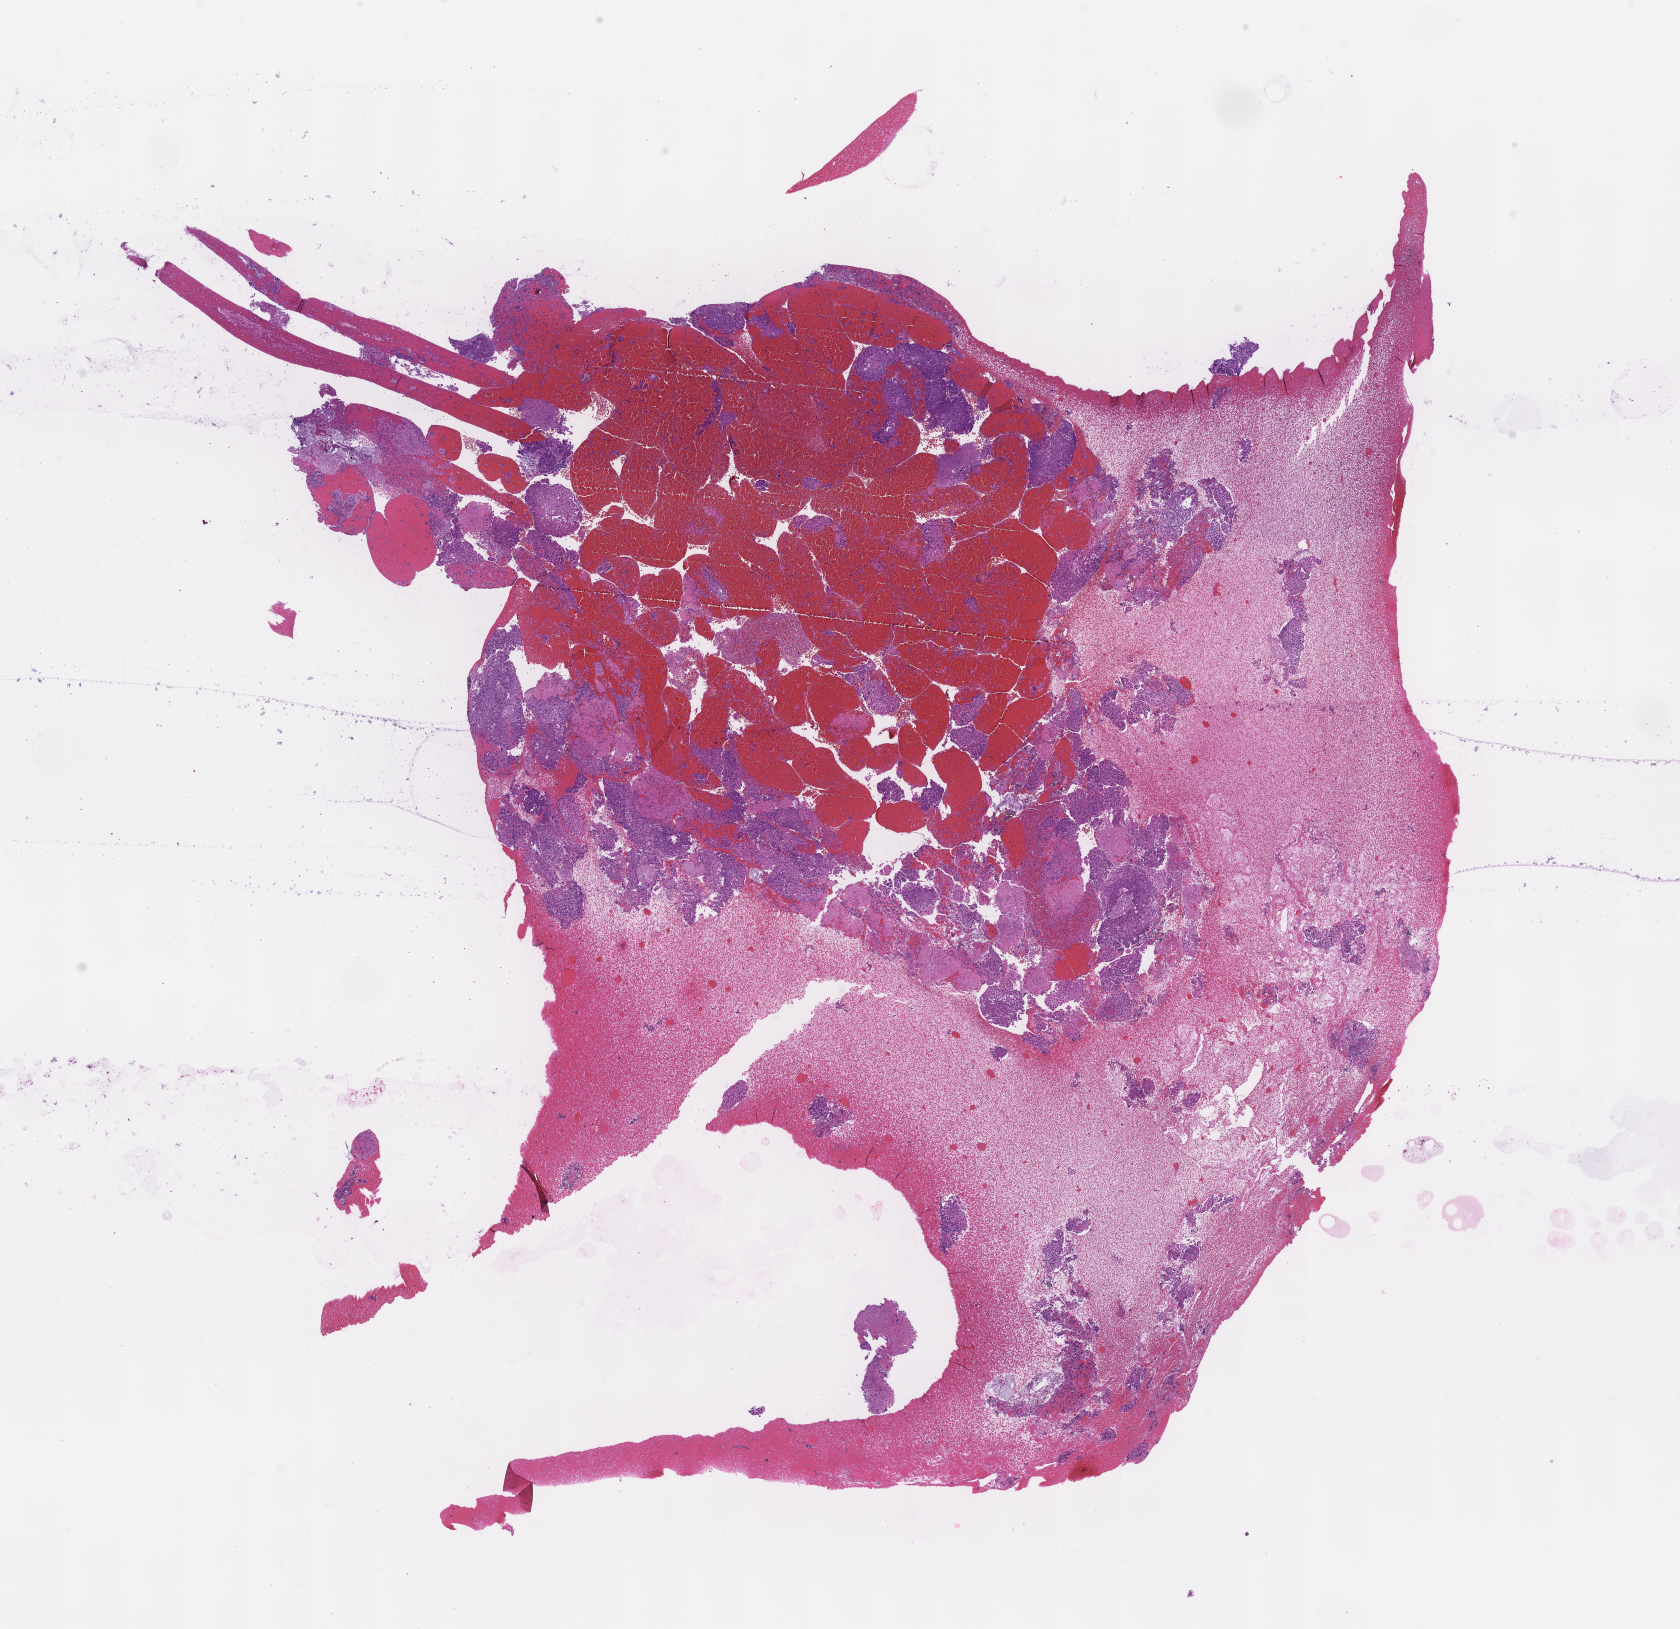
Digitized haematoxylin and eosin-stained section — a low-resolution overview of the entire scanned area, about 13.6 x 13.2 mm; formalin-fixed, paraffin-embedded (FFPE) tissue; site: lung; archival tissue. Male patient.
This section: primary tumor. Diagnosis: Non-Small Cell Lung Carcinoma.